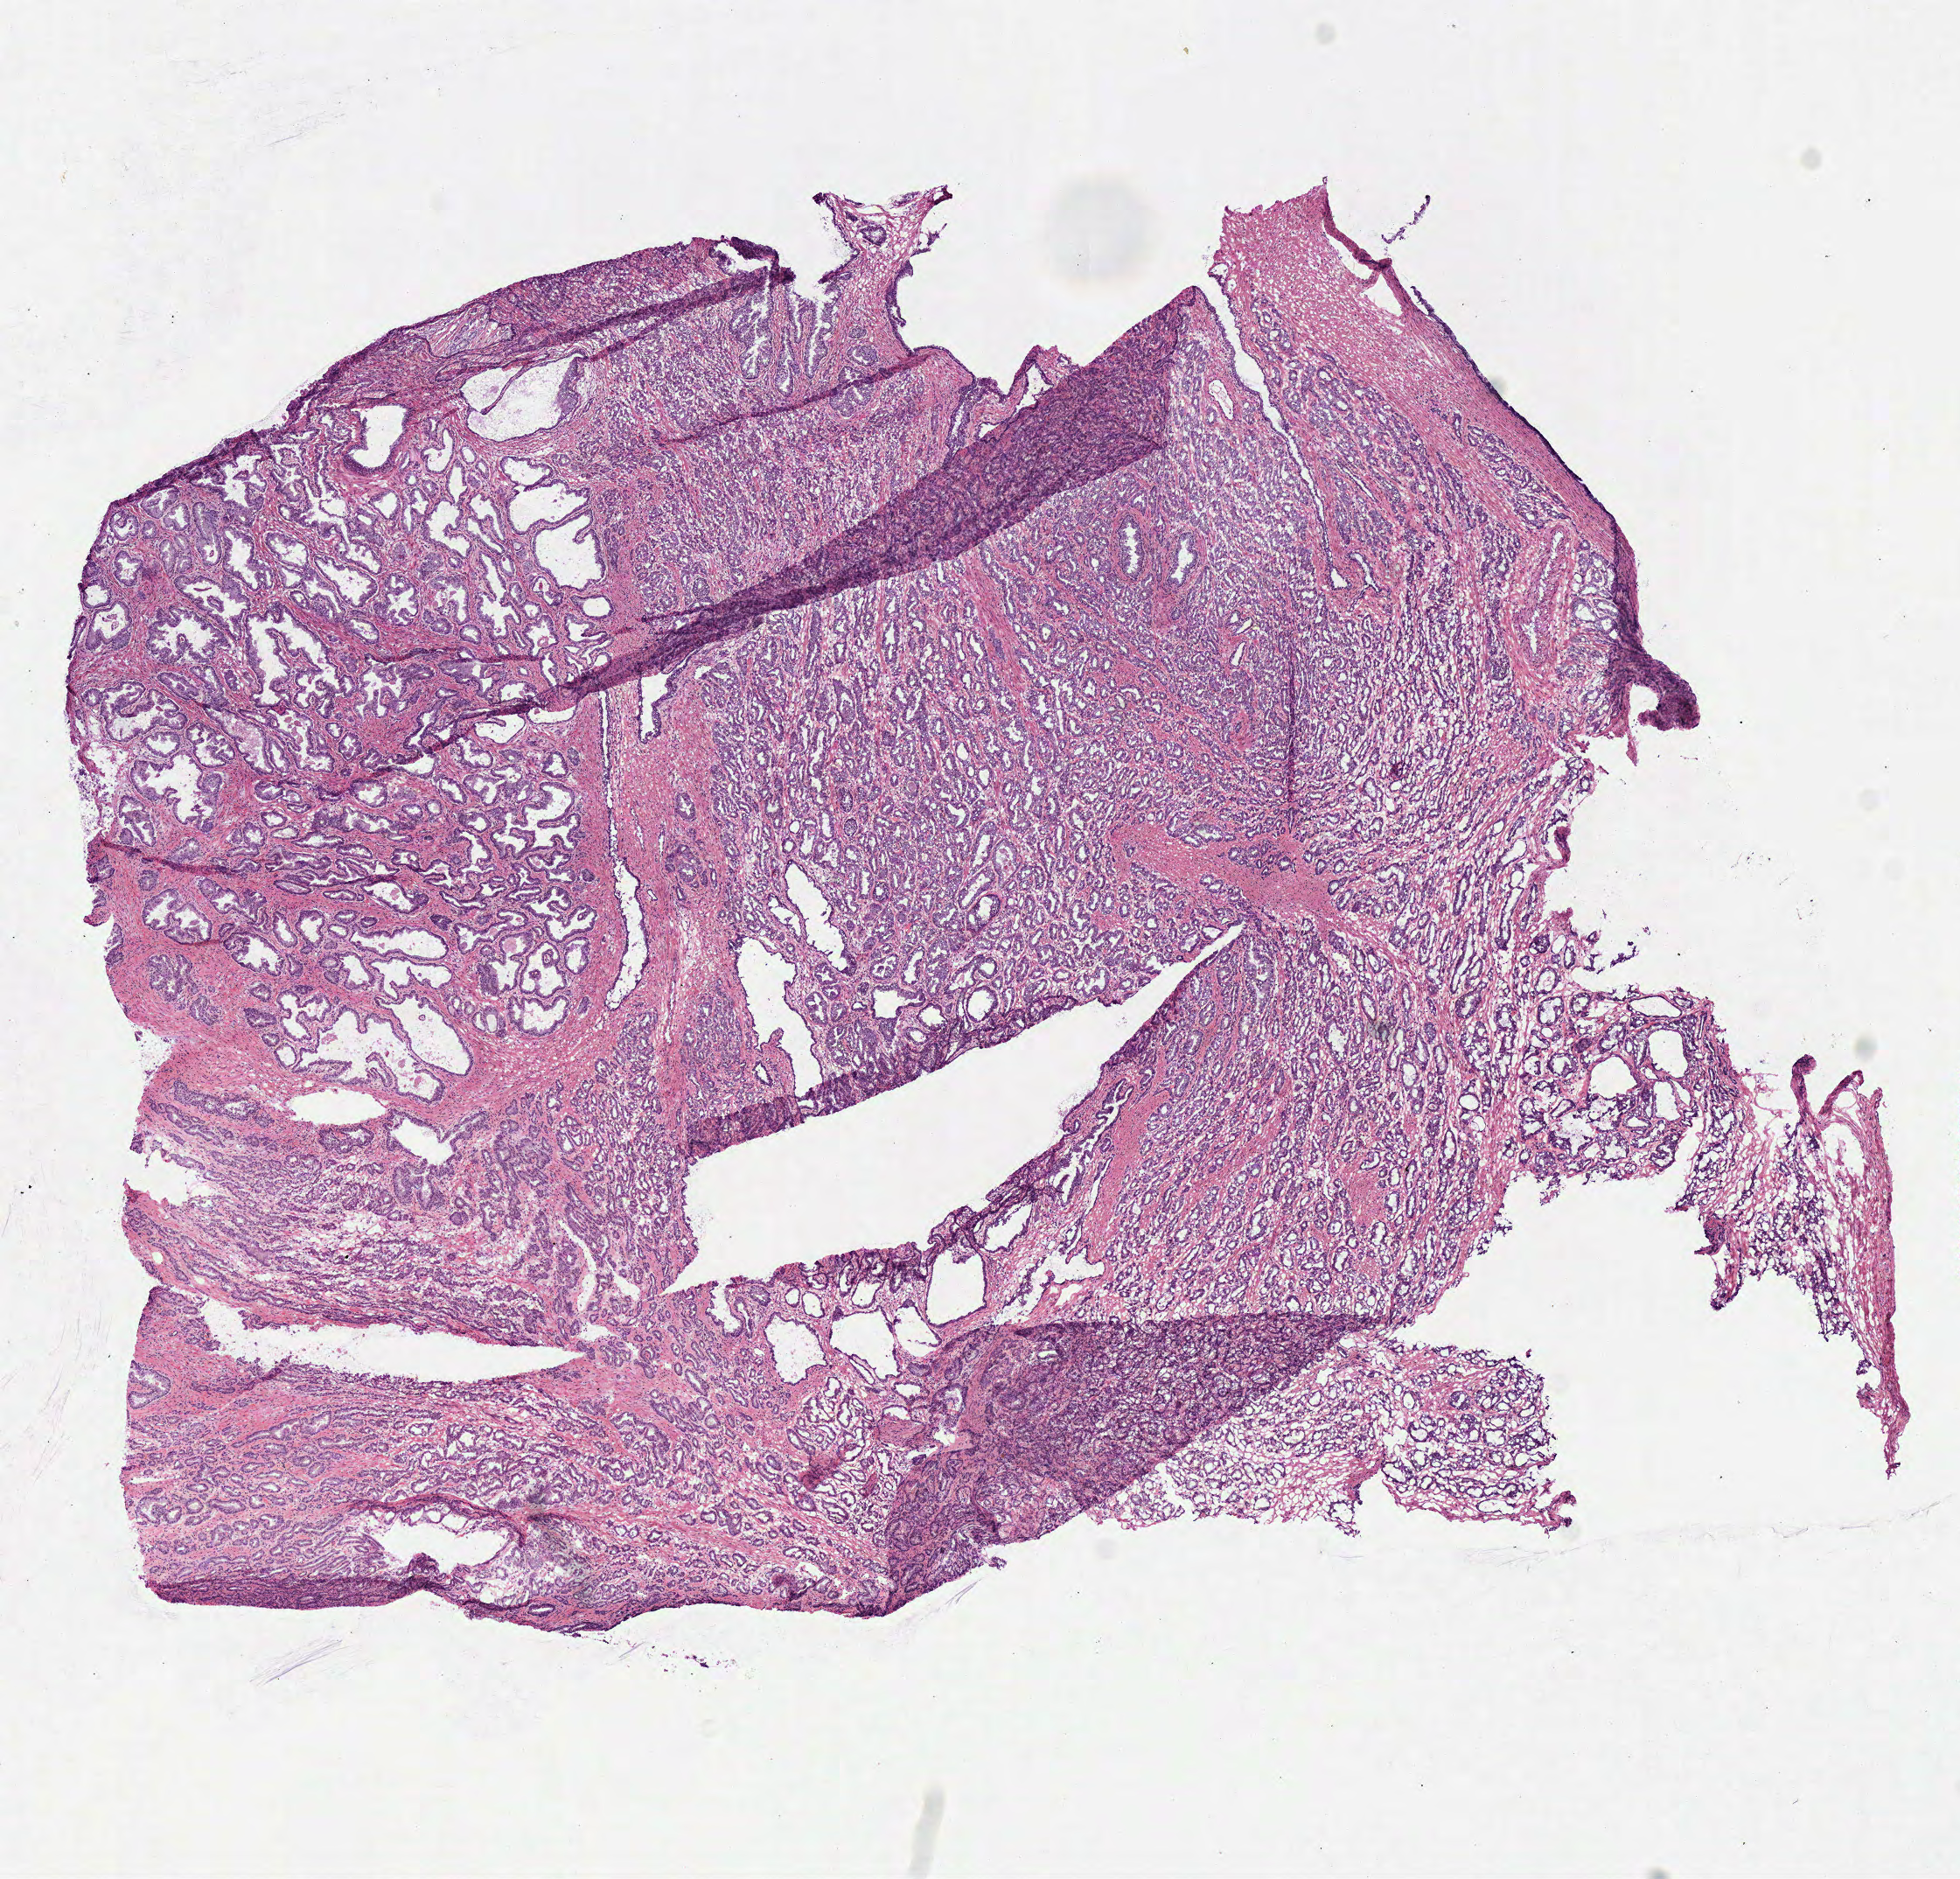
H&E-stained whole-slide image — a low-resolution overview of the entire scanned area, about 8.8 x 8.4 mm; frozen section from the top of the tissue portion; prostate, primary tumour sample. Male, age 54 years at initial diagnosis. Gleason score: 7 (3+4). Pathologist review of this section (percent, as recorded): tumour cells 75%, tumour nuclei 75%, normal cells 13%, stromal cells 12%, necrosis 0%. Infiltration values recorded for this section: lymphocyte infiltration 2%, monocyte infiltration 0%, neutrophil infiltration 0%.
Diagnosis: Acinar cell carcinoma (prostate gland). Laterality: bilateral.